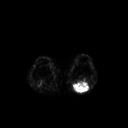
FDG PET of an extremity soft-tissue mass (from a PET/CT study), one axial slice. 3.27 mm slice thickness. 128 × 128 image matrix, field of view 500 × 500 mm. Male patient, age 54 years. Case-level facts recorded for this patient, not image findings: histological type: synovial sarcoma; site of the primary tumour: left poplietal fossa.
Structures marked on this image (expert contour drawn on MRI and transferred to this co-registered scan by the dataset authors):
- gross tumour volume (mass): box from (x=73, y=81) to (x=90, y=93) px